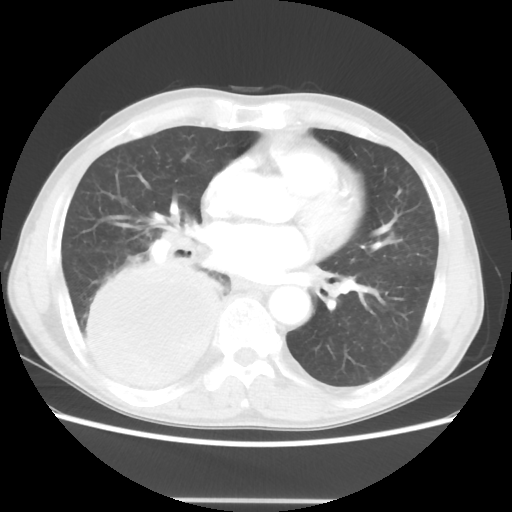
Chest CT, one axial slice. 100 kVp. Lung window (W 1500 / L -600 HU). 512 × 512 image matrix, field of view 361 × 361 mm. Male patient, age 66 years. From the clinical record (not read from this slice): clinical TNM (as recorded): T4 N1 M1.
Annotated regions visible in this slice (bounding box drawn by a radiologist):
- lung tumour (recorded histology: small cell carcinoma): bounding box [x1, y1, x2, y2] px = [69, 253, 221, 397]